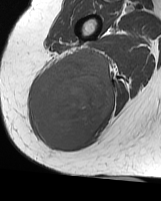
MRI of an extremity soft-tissue mass, one axial slice. Position 28 of 70 along the scan axis. MR volume resampled by the dataset authors to the PET/CT grid (not the native acquisition matrix). 161 × 201 image matrix. Female patient. From the clinical record (not read from this slice): histological type: synovial sarcoma; grade: intermediate; site of the primary tumour: right buttock.
Structures marked on this image (expert contour drawn on MRI and transferred to this co-registered scan by the dataset authors):
- gross tumour volume including surrounding oedema: bounding box <31,51,114,151> (left, top, right, bottom; pixels)
- gross tumour volume (mass): <31,51,114,151>